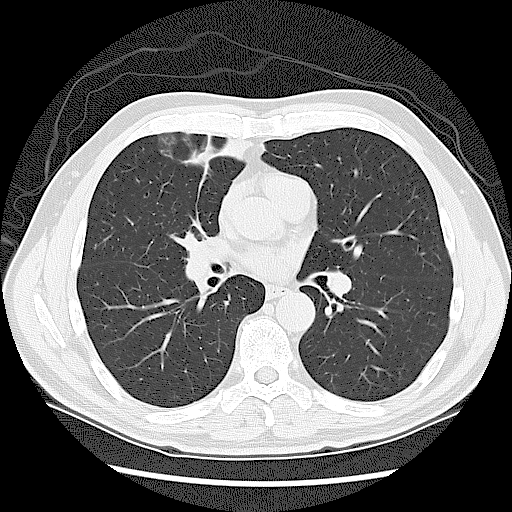
Chest CT (low-dose screening protocol), one axial image. Baseline screening round. Lung window (W 1500 / L -600 HU). Slice 66 of 131 in the series. Male participant, aged 60 years at enrolment. Current smoker at enrolment.
• Lesion marked by an expert reader, bounding box <157,212,239,301> (left, top, right, bottom; pixels).
• No non-calcified nodule or mass ≥4 mm was recorded by the screening reader at this exam.
• Official screen result: negative screen, significant abnormalities not suspicious for lung cancer.
• Later outcome: lung cancer diagnosed 41 days after this screen — small cell carcinoma, NOS, right upper lobe, stage IIIA (AJCC 6th edition).